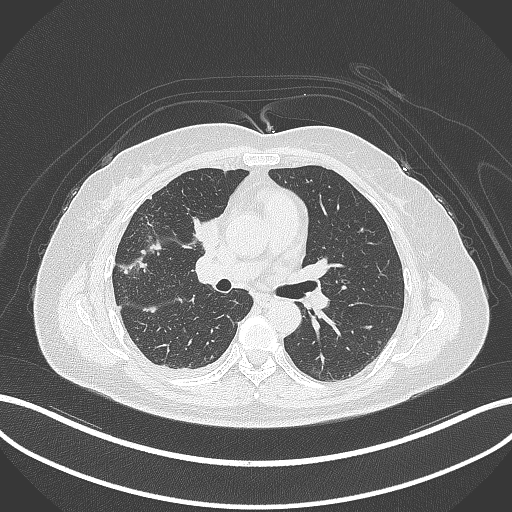
Chest CT, one axial slice; slice 154 of 305 in the series (ordered by position); 120 kVp; lung window (W 1500 / L -600 HU); 512 × 512 image matrix. Female patient, age 52 years. Case-level facts recorded for this patient, not image findings: clinical TNM (as recorded): T3 N1 M1.
Outlined on this slice (bounding box drawn by a radiologist):
- lung tumour (recorded histology: adenocarcinoma): box from (x=189, y=211) to (x=222, y=256) px